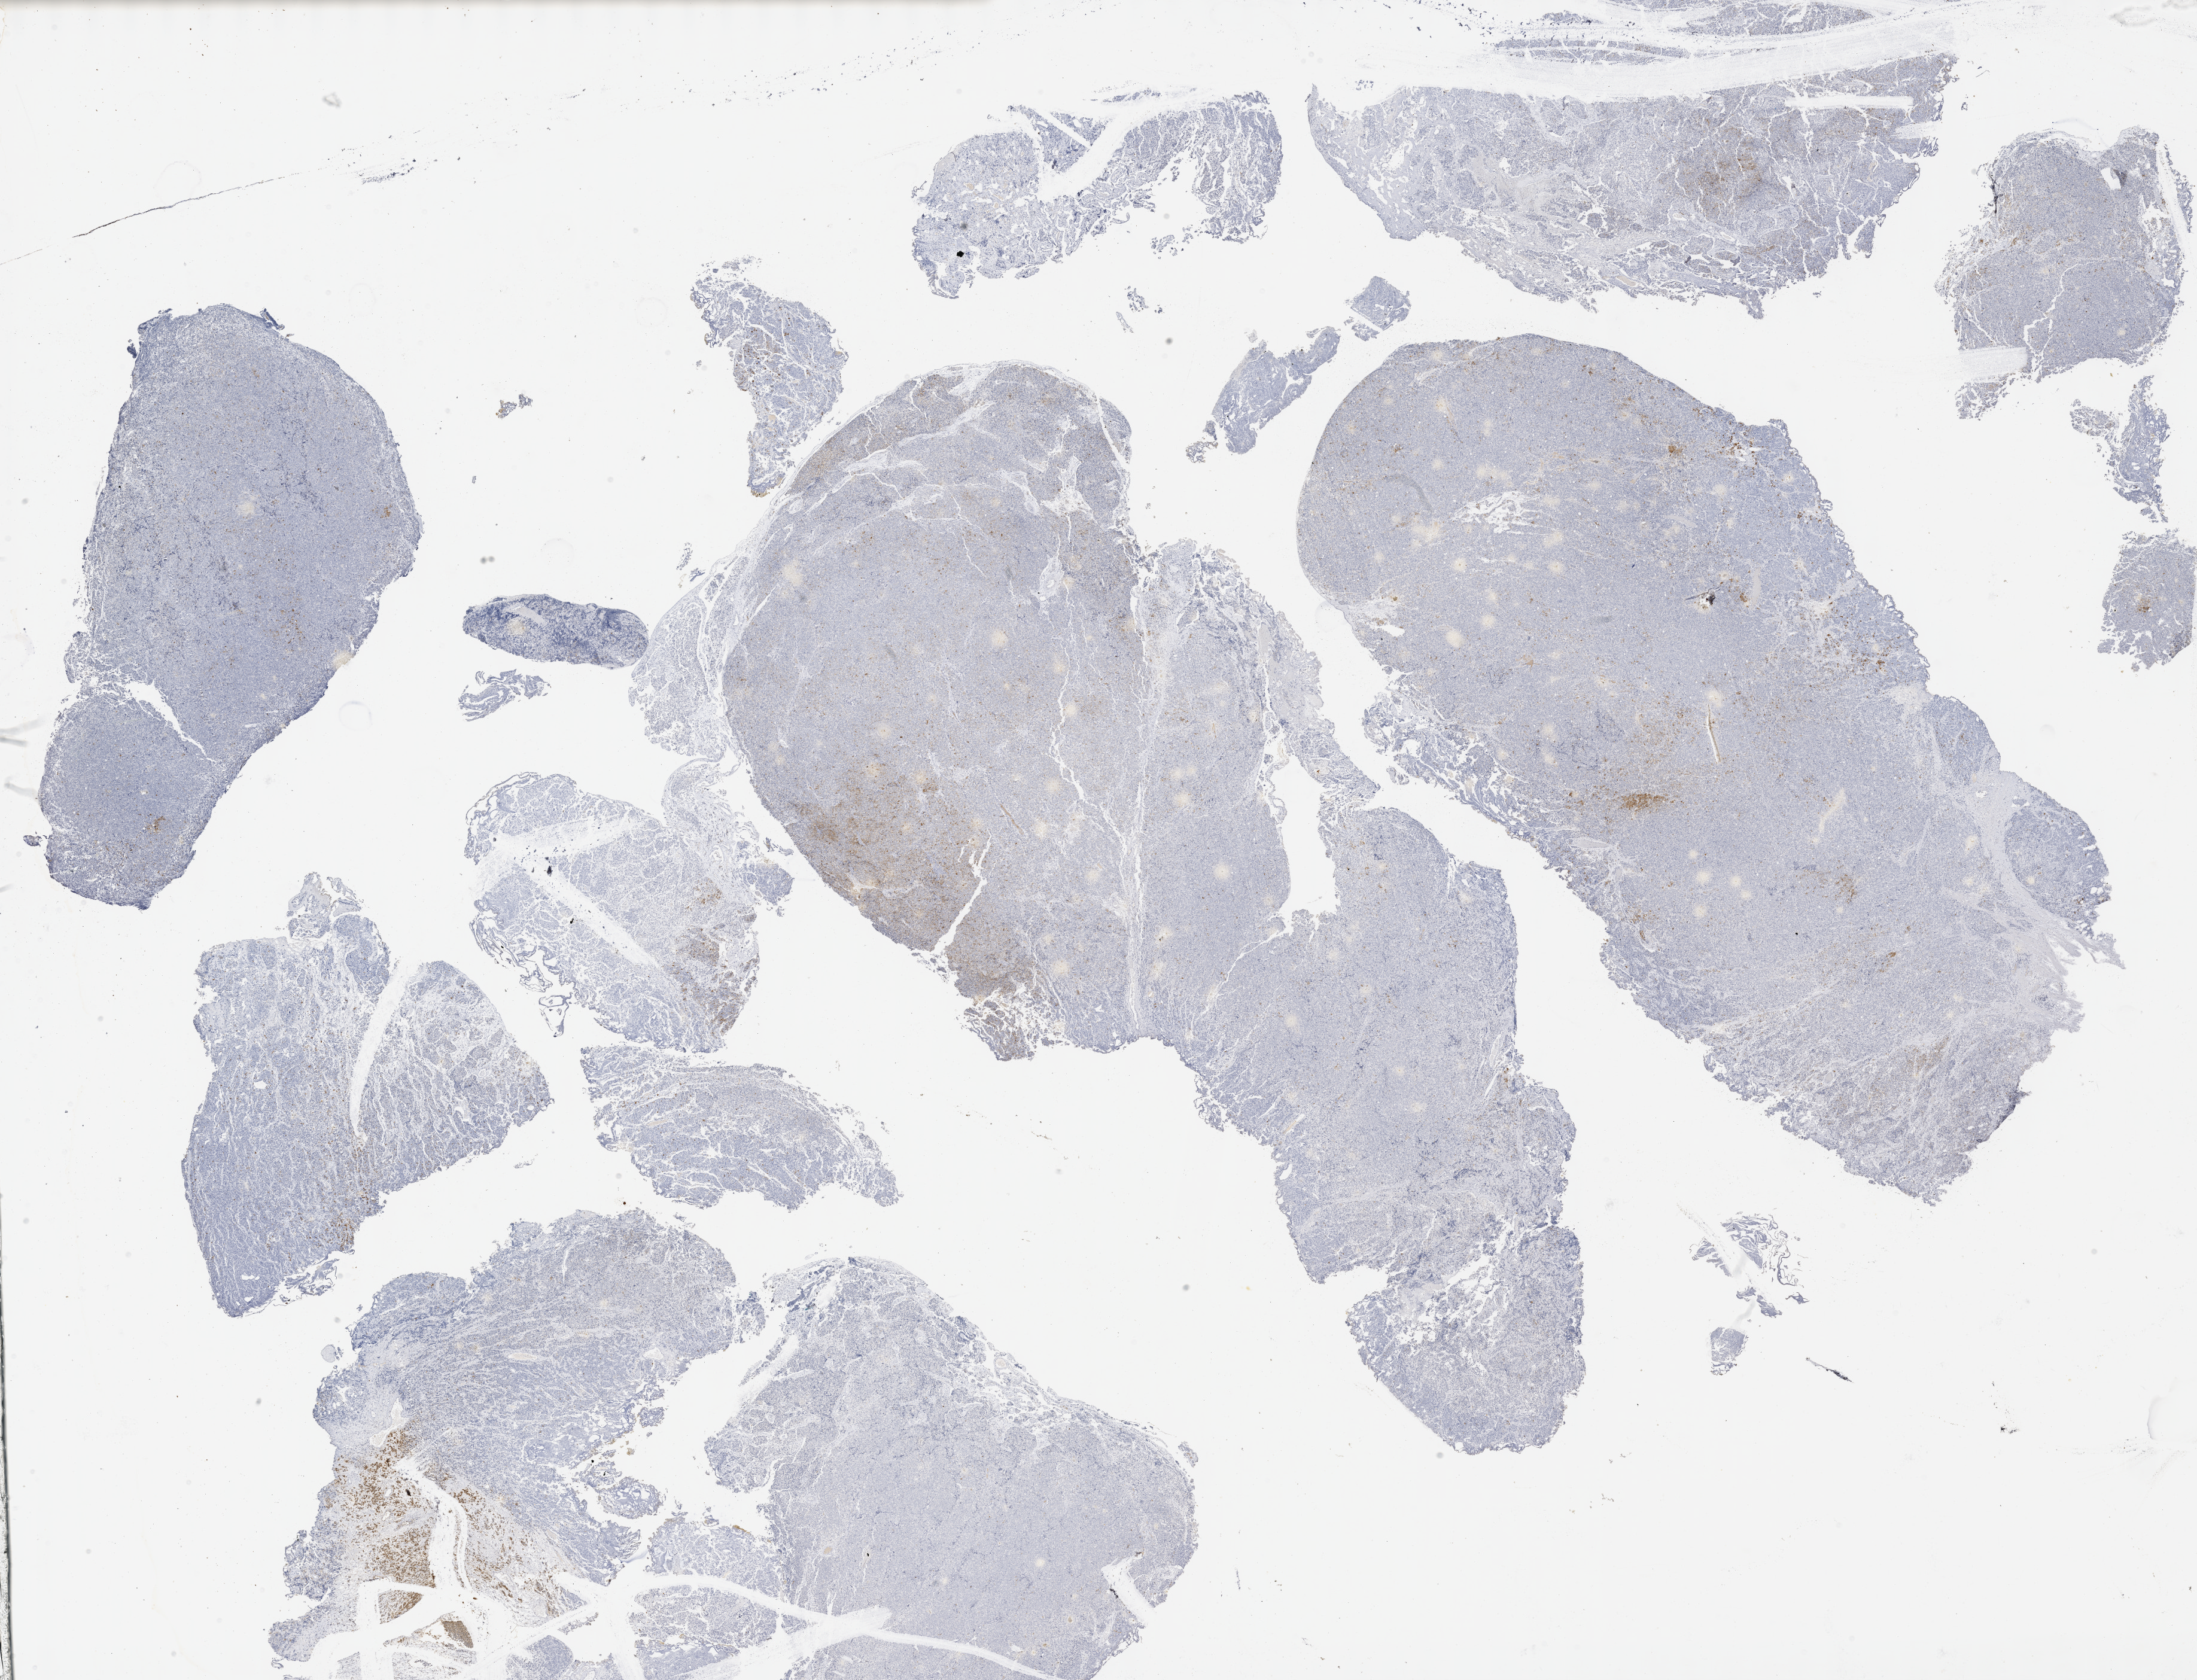
Digitized Hematoxylin and eosin (H&E) stained tissue section (whole slide) — whole scanned area (about 29.7 x 22.7 mm, acquisition: 40x scan) shown as a low-resolution overview; formalin-fixed paraffin-embedded (FFPE) diagnostic section; prostate, primary tumour sample. Patient: male, age at initial diagnosis 59 years. Gleason score: 10 (5+5).
* histologic diagnosis: Adenocarcinoma, NOS (prostate gland)